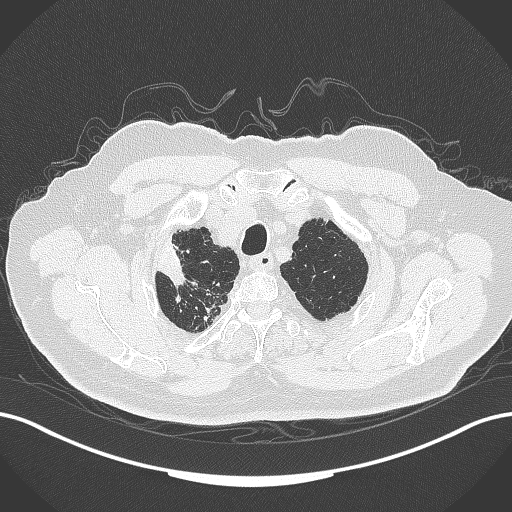
Chest CT, one axial slice; position 316 of 389 along the scan axis; reconstruction kernel B70f; 120 kVp; lung window (W 1500 / L -600 HU); 1 mm slice thickness; 512 × 512 image matrix, field of view 400 × 400 mm. Patient: male, 72 years. Case-level facts recorded for this patient, not image findings: clinical TNM (as recorded): T1a N0 M0.
Structures marked on this image (rectangle marked by the reading radiologist):
- lung tumour (recorded histology: squamous cell carcinoma): bounding box (x1, y1, x2, y2) in pixels: (155, 235, 188, 290)